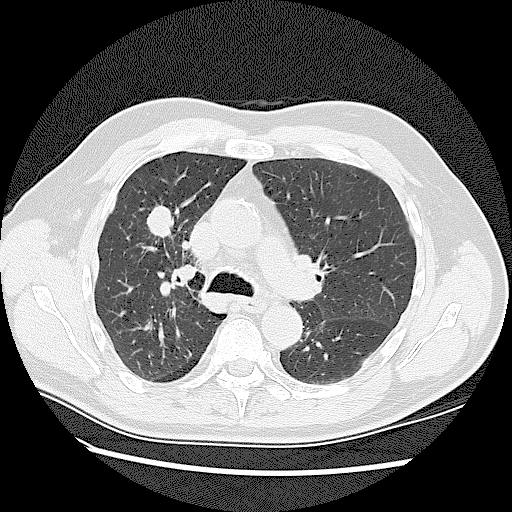
Axial slice from a low-dose chest CT screening exam; baseline screening round; lung window (W 1500 / L -600 HU); slice 47 of 128 in the series. Male participant, aged 72 years at enrolment. Current smoker at enrolment.
• Expert-annotated lung lesion, box from (x=133, y=200) to (x=181, y=239) px.
• The screening reader recorded 2 non-calcified nodules or masses ≥4 mm on this exam (right upper lobe, right upper lobe); which of them this box marks is not recorded.
• Official screen result: positive, change unspecified: nodule(s) >= 4 mm or enlarging nodule(s), mass(es), or other non-specific abnormalities suspicious for lung cancer.
• Later outcome: lung cancer diagnosed 42 days after this screen — adenocarcinoma, NOS, right upper lobe, stage IV (AJCC 6th edition), 45 mm at pathology.